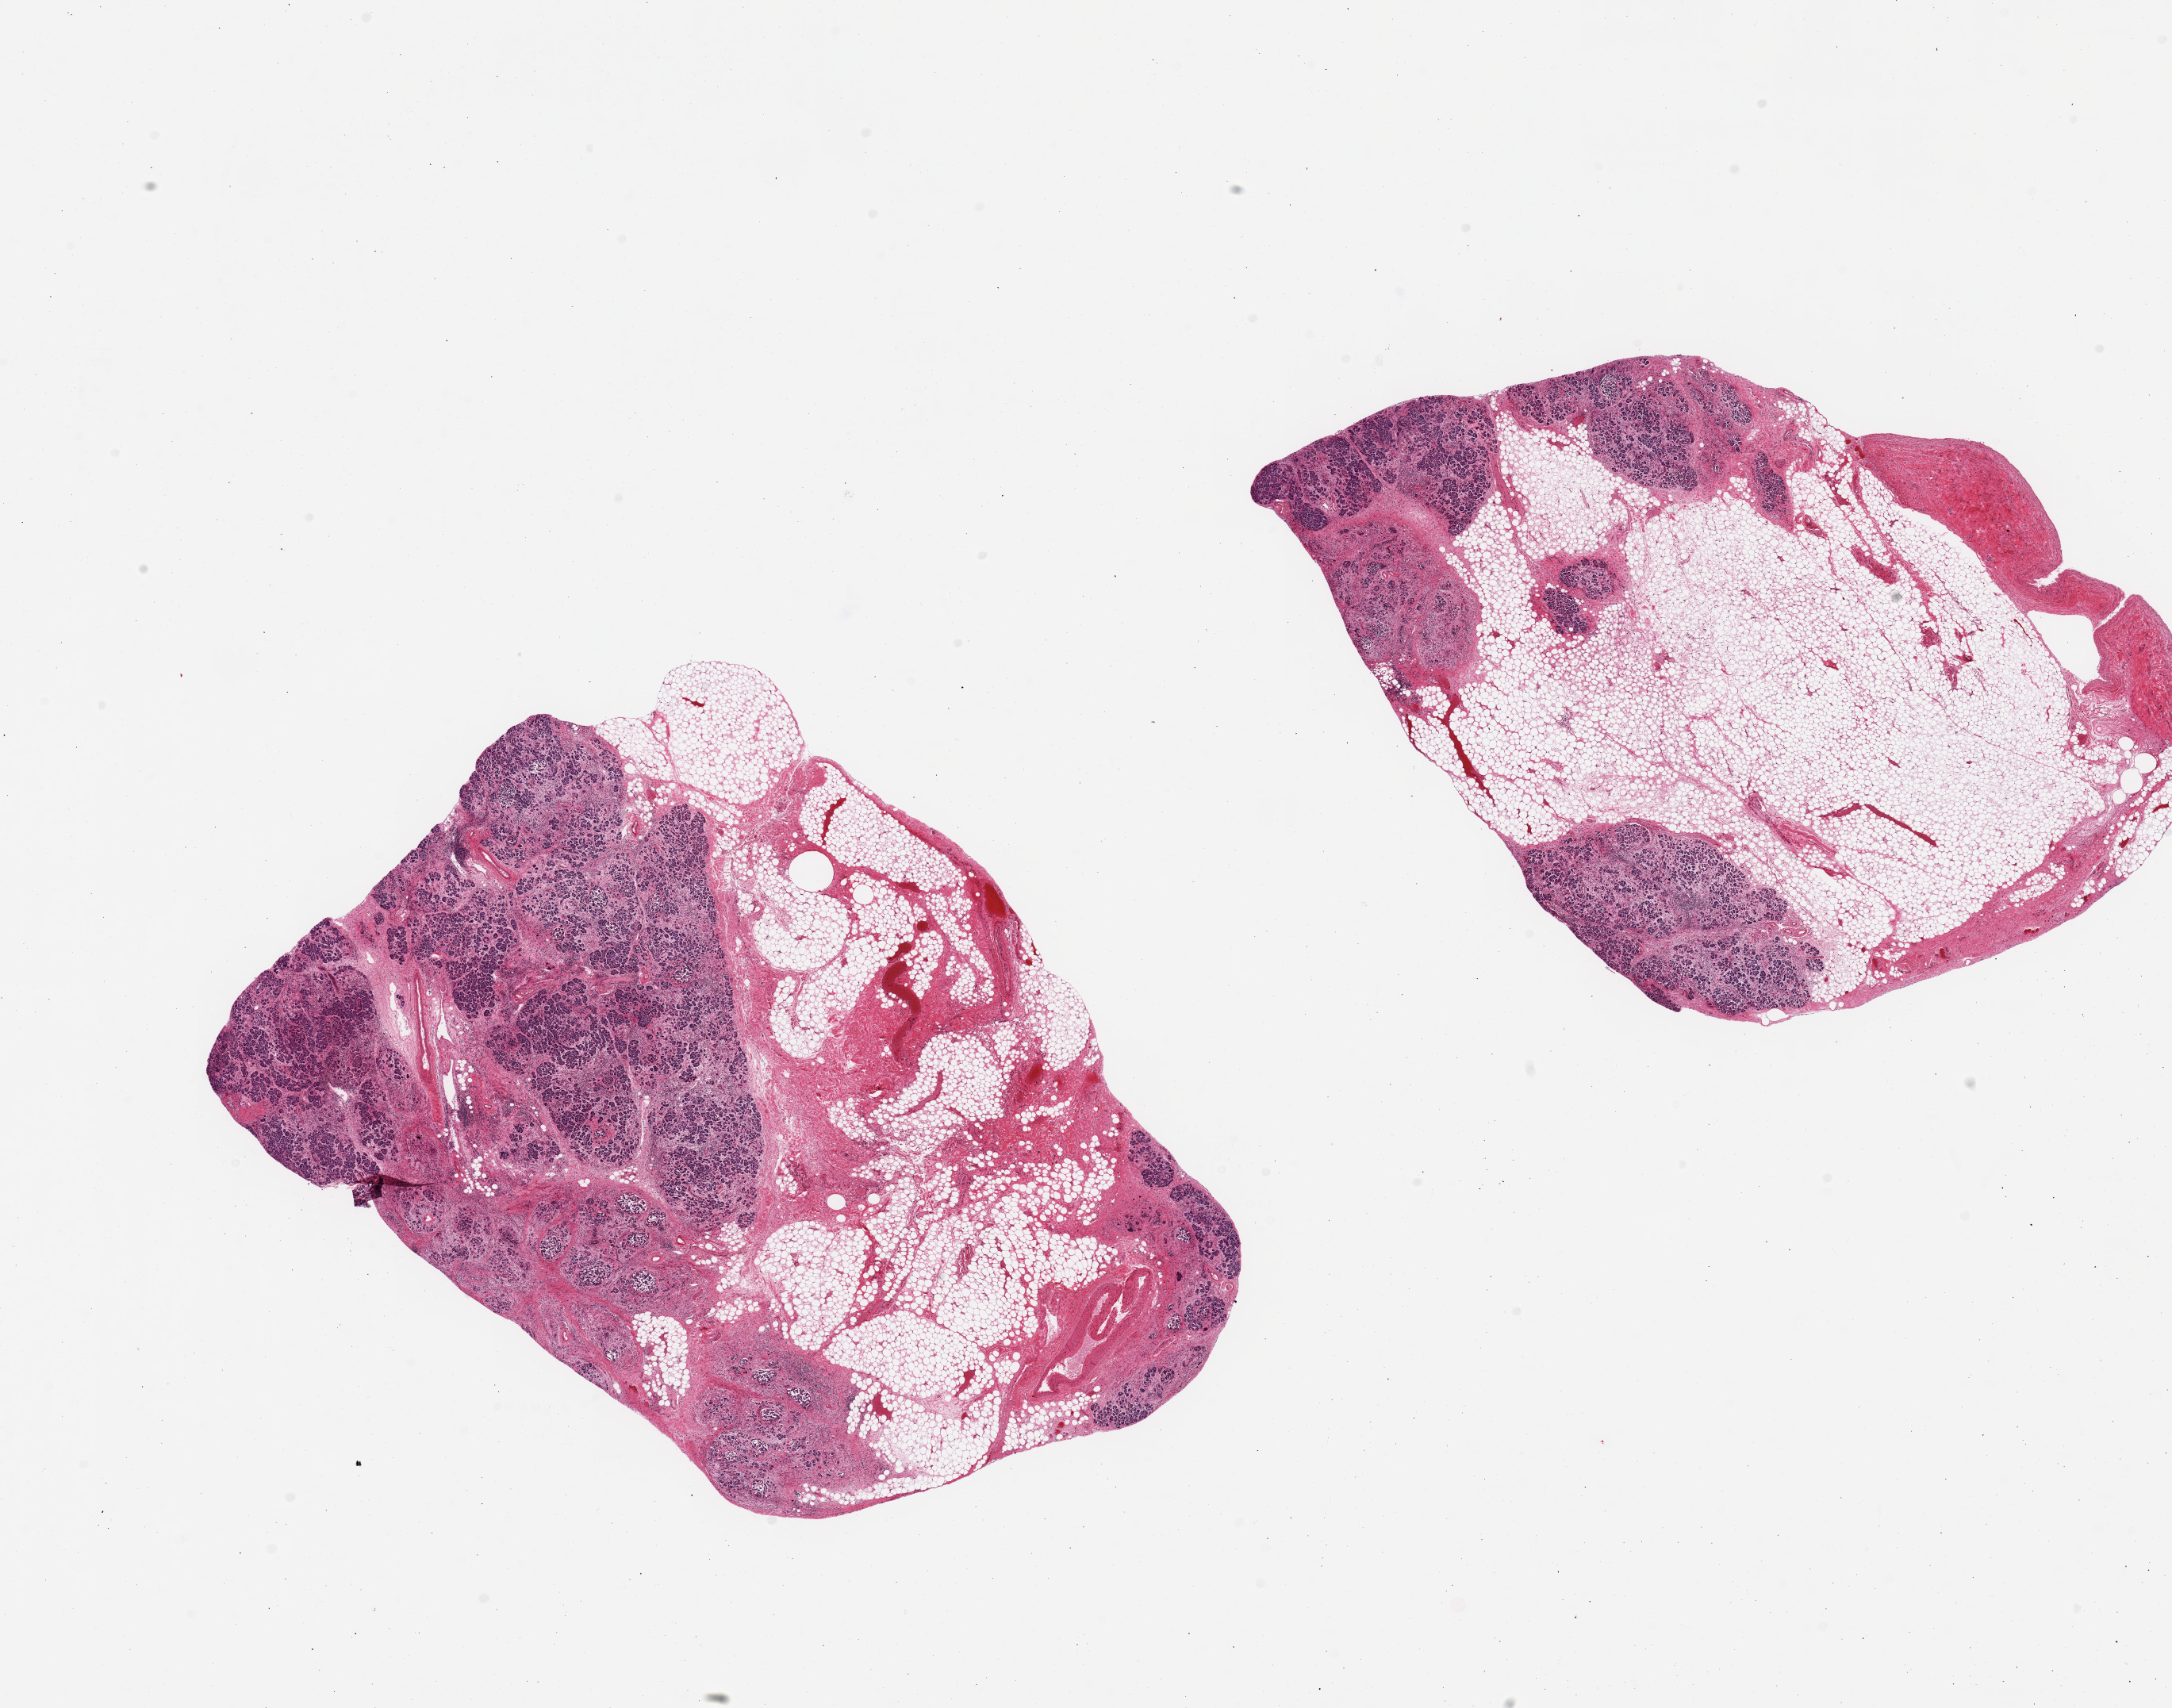
Digitized hematoxylin and eosin (H&E)-stained section — low-resolution overview of the scanned area, about 21.7 x 17.0 mm (from a 20x scan). PAXgene-fixed, paraffin-embedded tissue. Sampled site (target tissue): pancreas. Donor tissue sample. Female donor.
- review note (as recorded): 2 pieces; chronic inflammation, fibrosis and atrophy; 60% fat content